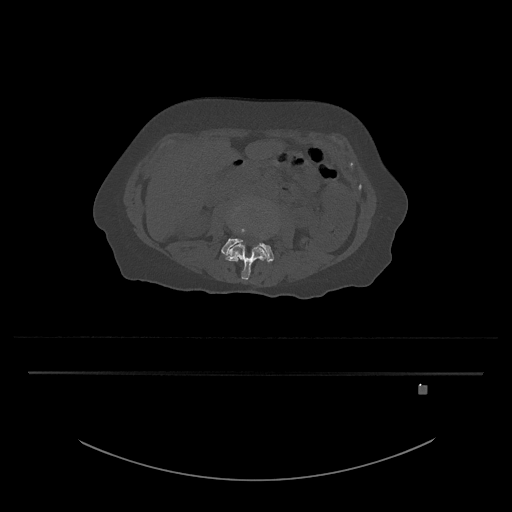
CT including the spine, one axial slice; position 398 of 797 along the scan axis; reconstruction kernel Br40s/3; 120 kVp; bone window (W 1800 / L 400 HU); 512 × 512 image matrix, field of view 500 × 500 mm. Patient: female, 57 years. From the clinical record (not read from this slice): primary cancer: cervical.
Annotated regions visible in this slice (semi-automatic segmentation, software-assisted and operator-edited):
- L3 vertebra: bounding box <225,229,267,280> (left, top, right, bottom; pixels)
- L4 vertebra: <221,214,274,263>